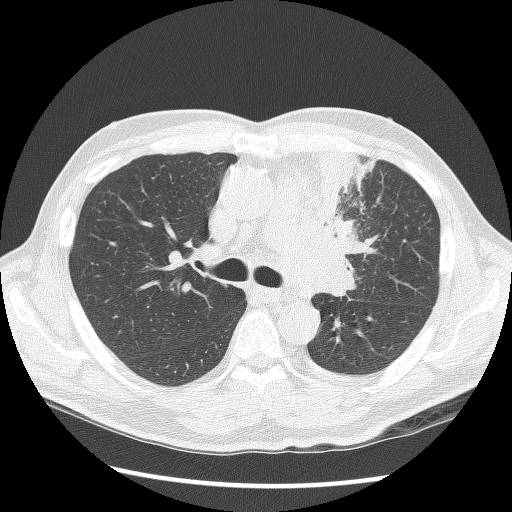
Low-dose screening chest CT, axial slice. Second screening round (one year after baseline). Lung window (W 1500 / L -600 HU). Lung (sharp) reconstruction kernel (BONE). 120 kVp. Male, age 64 years at enrolment. Former smoker at enrolment.
Expert reader's lesion annotation, bounding box [x1, y1, x2, y2] px = [301, 153, 379, 285]. Screening reader's record for this exam: no non-calcified nodule ≥4 mm recorded. Official screen result: positive, other. Participant outcome: lung cancer diagnosed 24 days after this screen — small cell carcinoma, NOS, left upper lobe, stage IV (AJCC 6th edition), 100 mm at pathology.